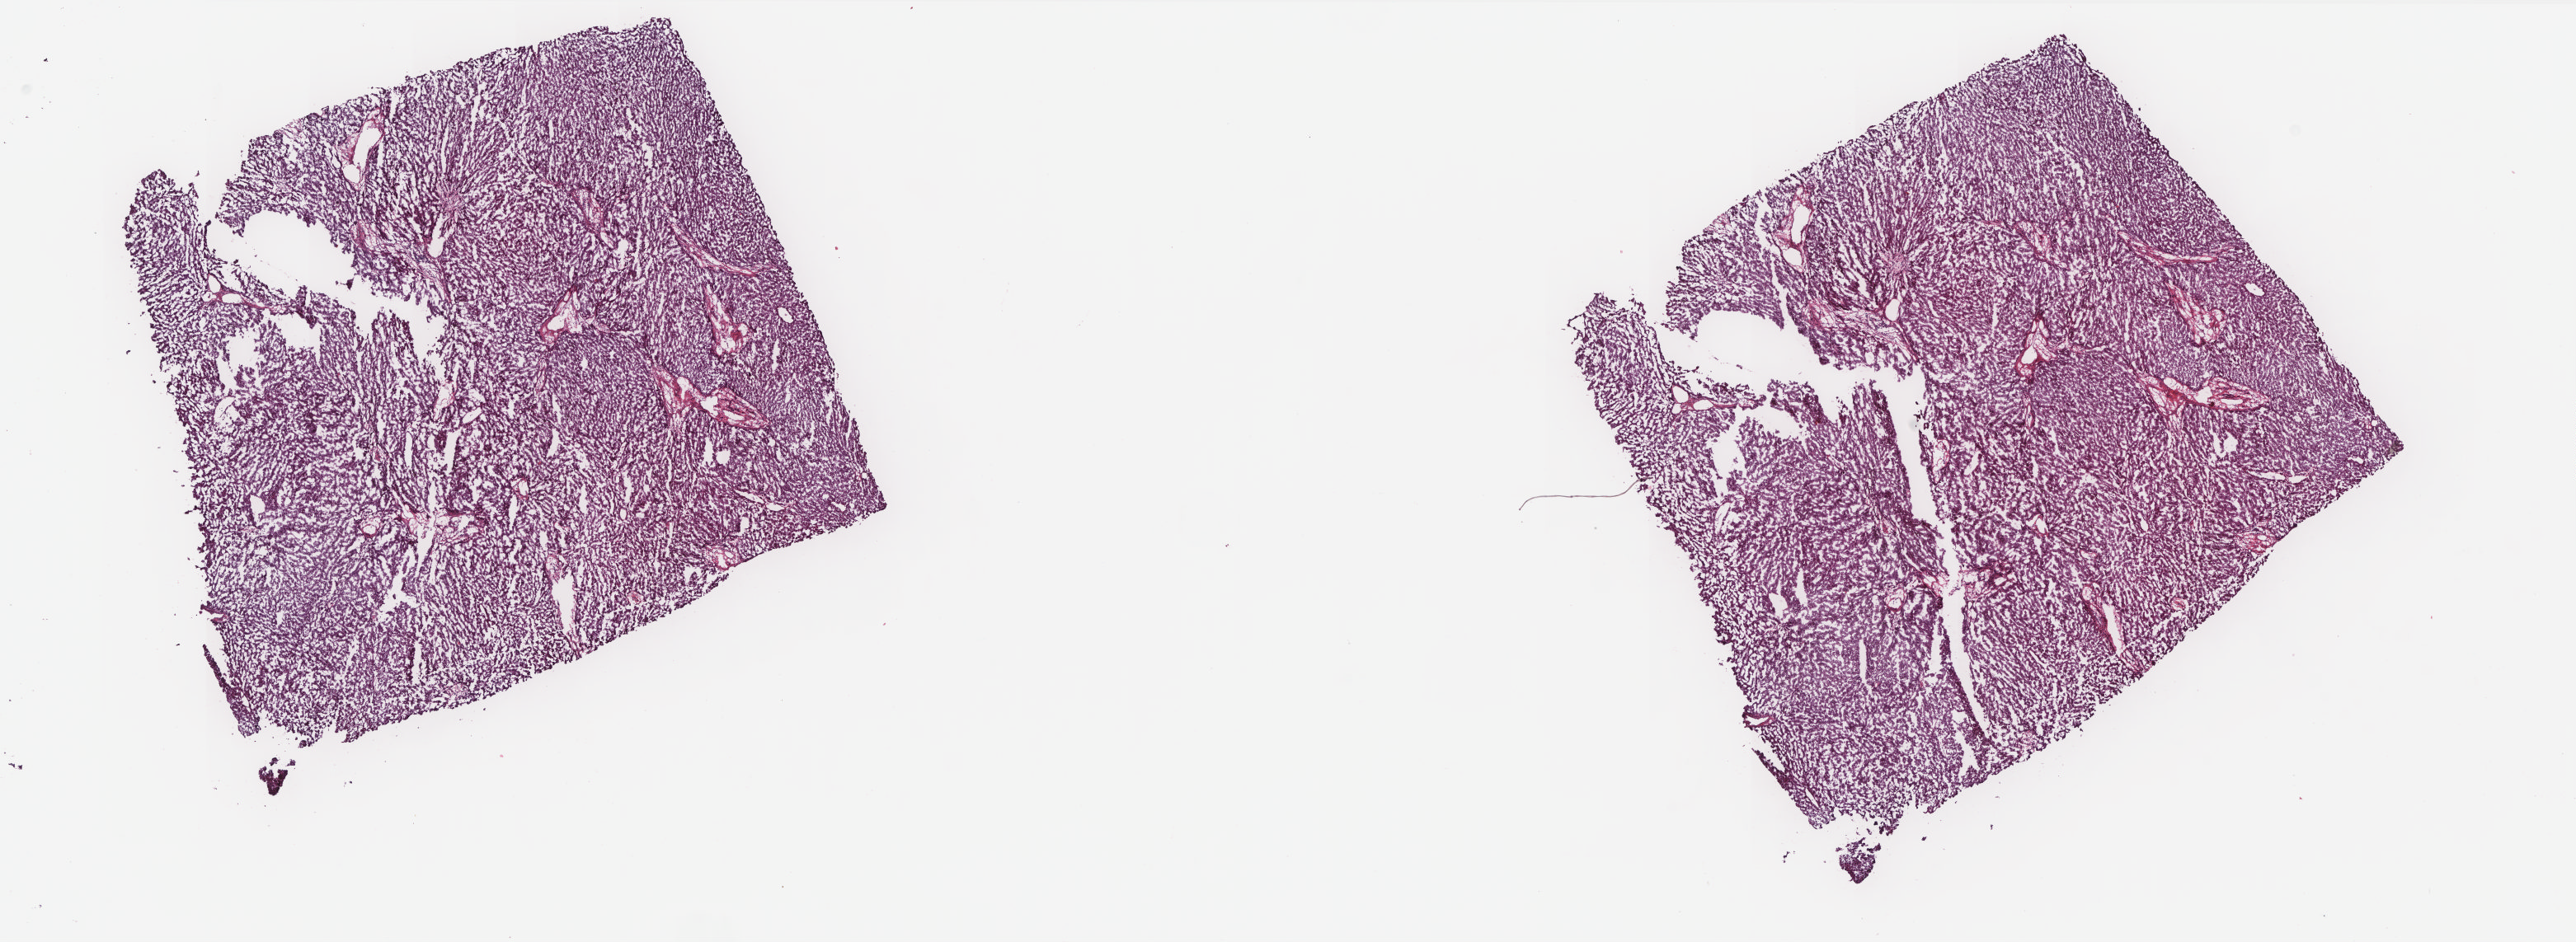
Digitized H&E tissue section (whole slide), whole scanned area (about 25.0 x 9.1 mm, slide scanned at 20x) shown as a low-resolution overview. Frozen section from the top of the tissue portion. Sample: solid tissue normal (non-tumour tissue), liver. Patient: male, age at initial diagnosis 75 years.
This section: solid tissue normal sample (biorepository sample class). Patient diagnosis: Hepatocellular carcinoma, NOS.